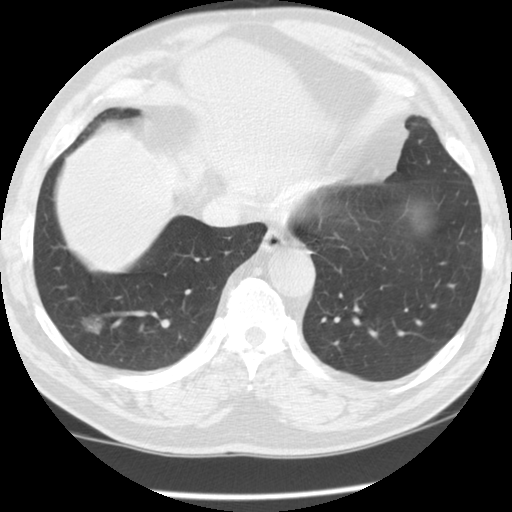
Low-dose screening chest CT, axial slice; second annual screen; lung window (W 1500 / L -600 HU); 2.5 mm slice thickness; standard (soft-tissue) reconstruction kernel (STANDARD); 120 kVp; slice 88 of 115 in the series. Male, age 62 years at enrolment. Former smoker at enrolment.
Expert-annotated lung lesion, bounding box <65,304,124,357> (left, top, right, bottom; pixels). Screening reader's record for this exam (one nodule recorded; not confirmed to be the boxed lesion): non-calcified nodule or mass ≥4 mm, right lower lobe, 13 × 11 mm, smooth margins, ground glass attenuation, pre-existing on the prior screen: yes; interval growth: no.